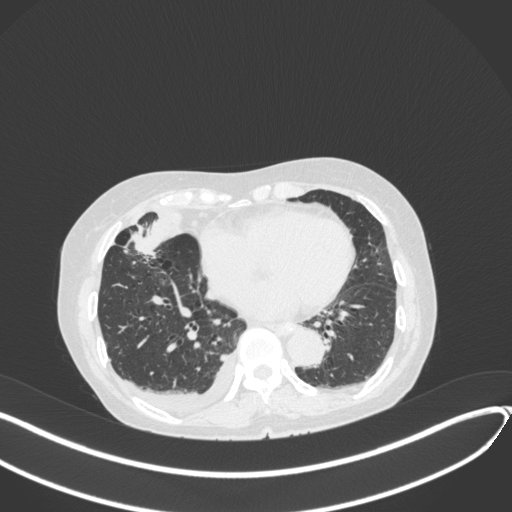
Chest CT, one axial slice. Position 140 of 418 along the scan axis. Reconstruction kernel B31f. 120 kVp. Lung window (W 1500 / L -600 HU). 1 mm slice thickness. 512 × 512 image matrix, field of view 400 × 400 mm. Patient: female, 75 years. From the clinical record (not read from this slice): clinical TNM (as recorded): T2a N3 M0.
Structures marked on this image (bounding box drawn by a radiologist):
- lung tumour (recorded histology: adenocarcinoma): bounding box <122,221,162,257> (left, top, right, bottom; pixels)